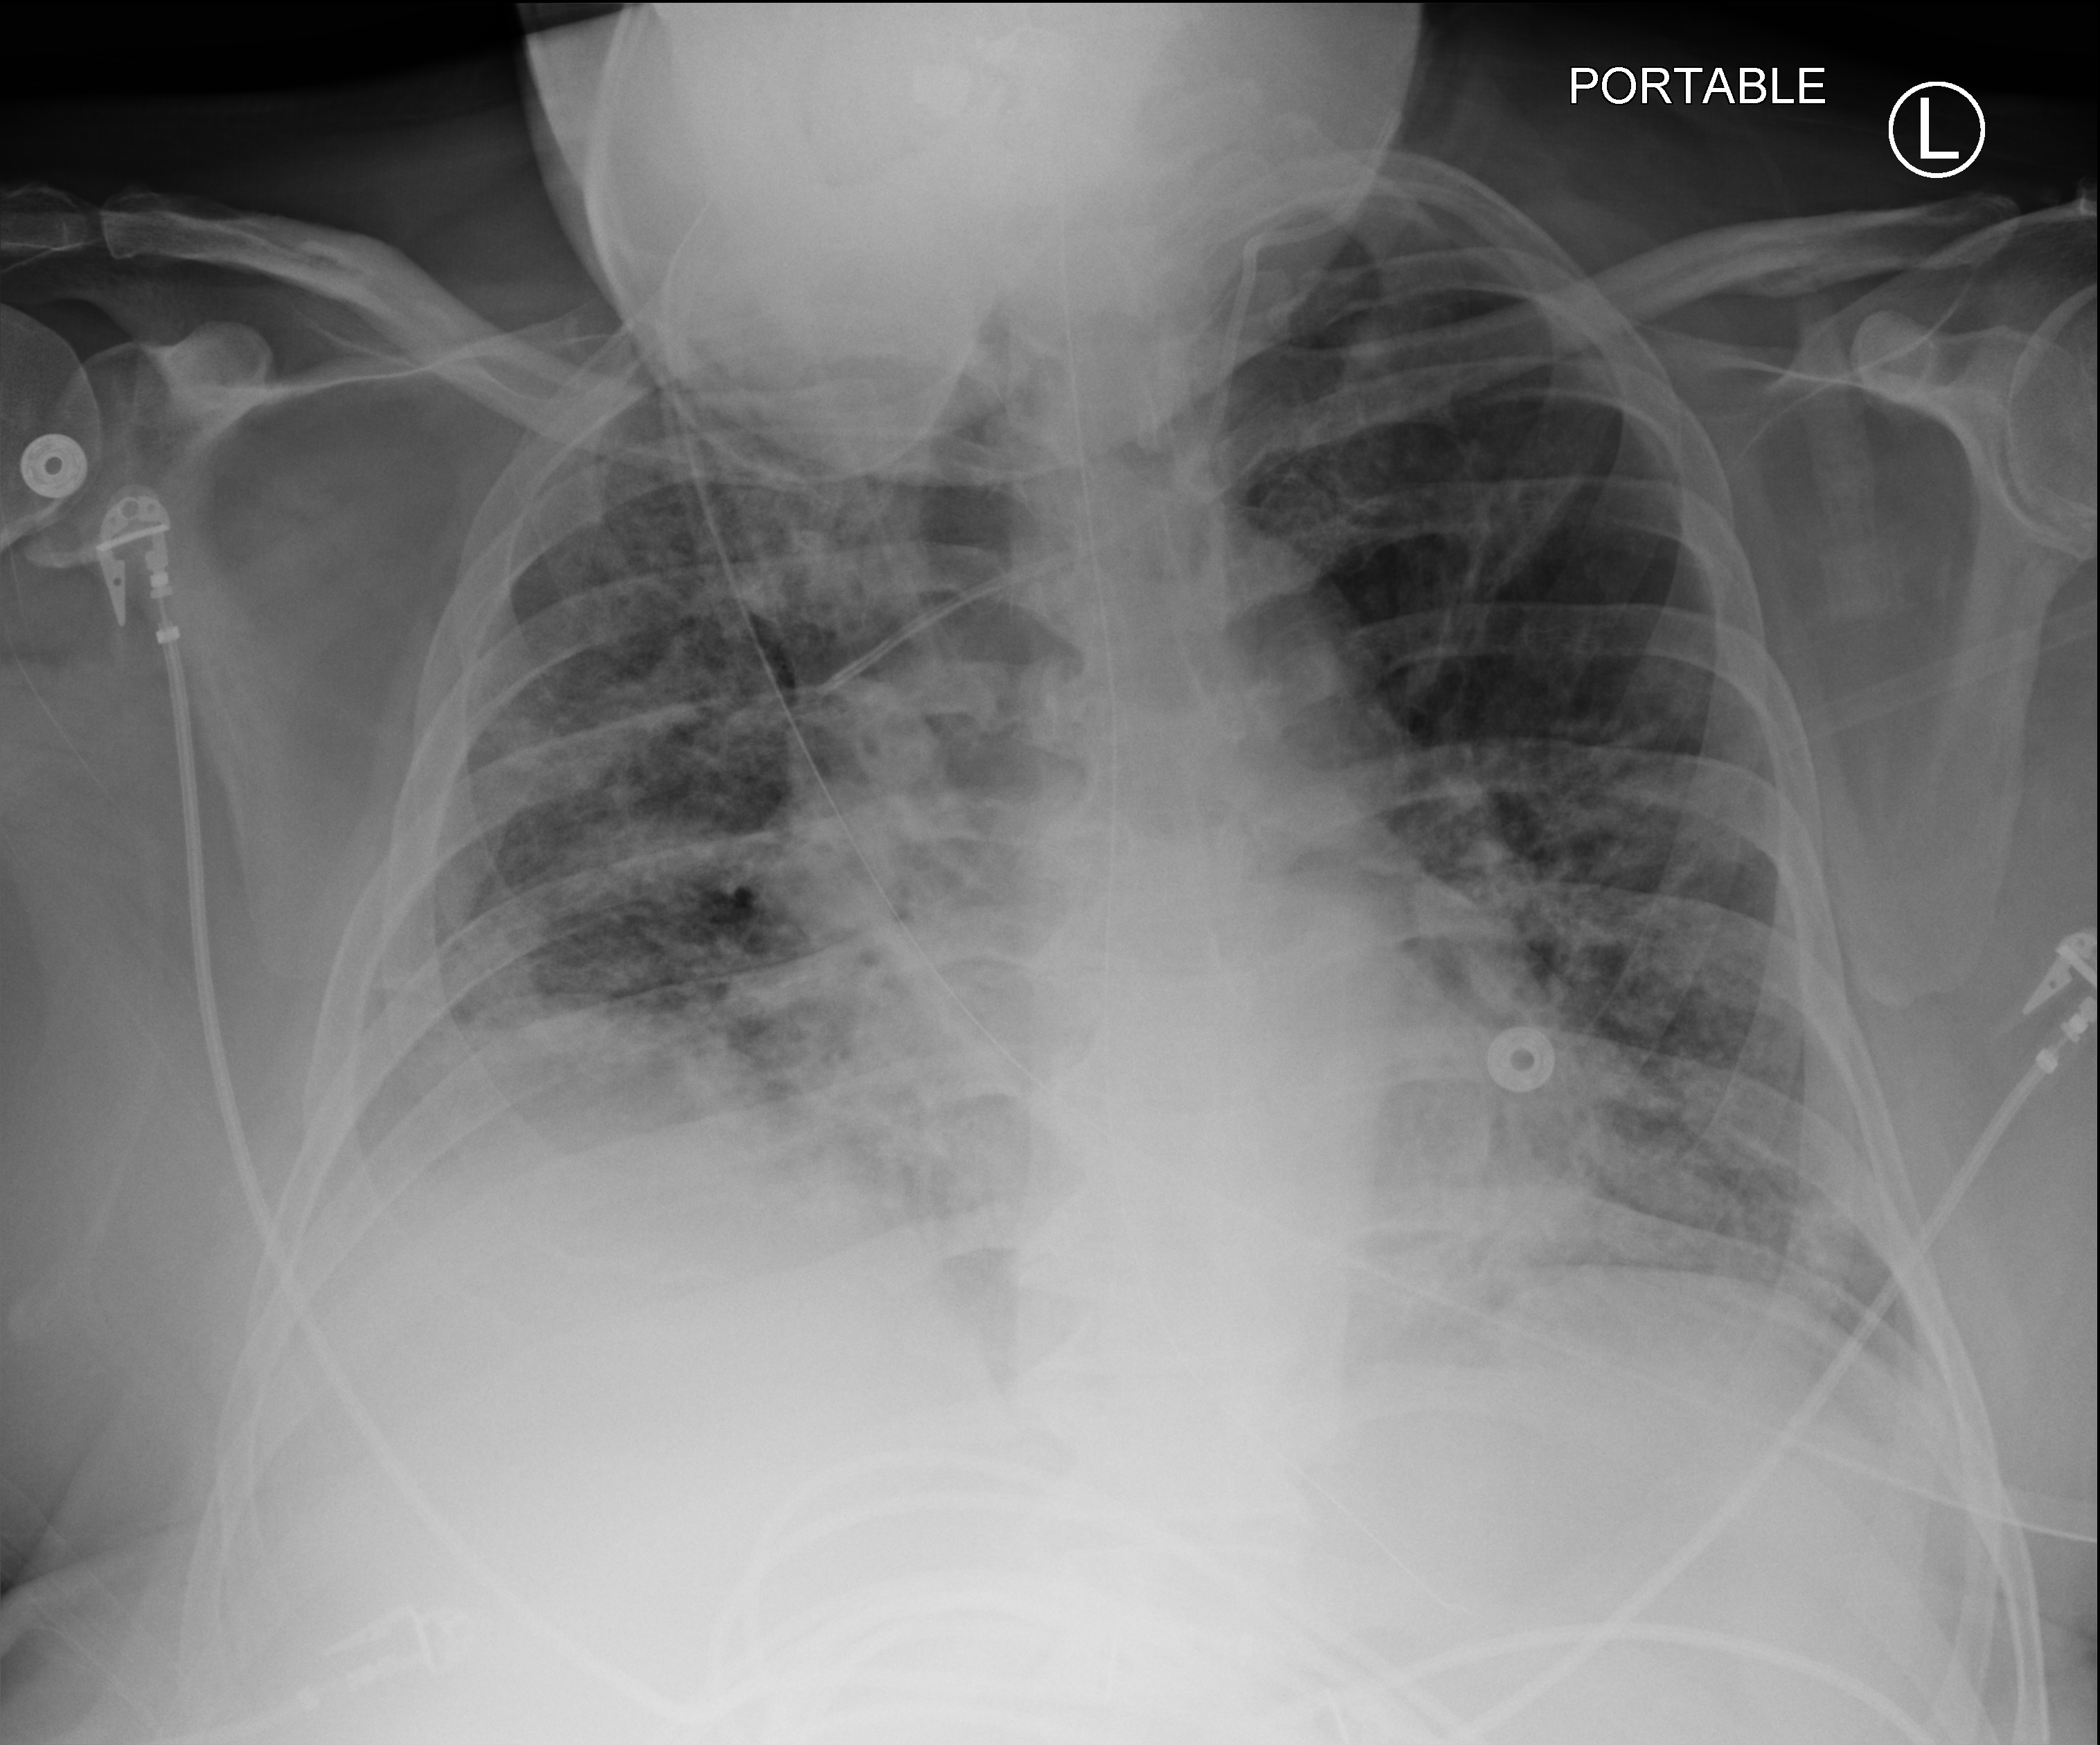
Bedside chest radiograph (computed radiography); anteroposterior (AP) projection. Patient hospitalised with COVID-19; male, aged 18–59 years.
Admission-level facts for this patient (not findings on this image; timing relative to this image not recorded): admitted to intensive care during this hospital stay: yes.